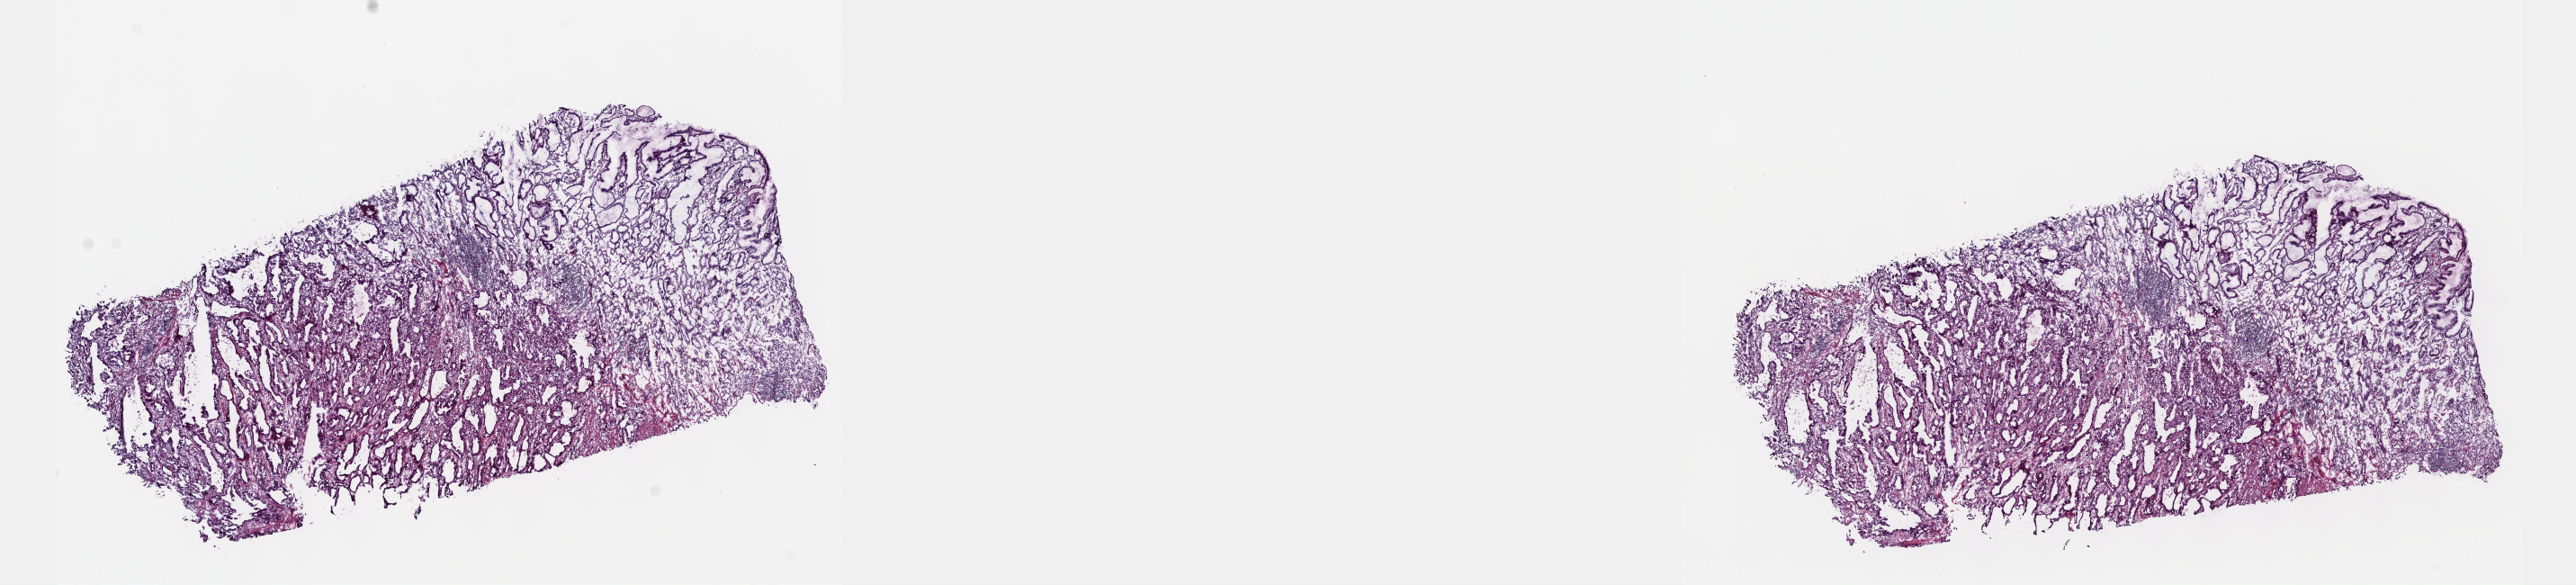
Digitized H&E tissue section (whole slide), shown as a low-resolution overview of the whole scanned area (about 23.1 x 5.3 mm, from a 40x scan); frozen section; primary tumour sample from the stomach. Male, age 76 years at initial diagnosis. Histologic grade: G2 (moderately differentiated). Composition of this section per pathologist review: tumour cells 100%, tumour nuclei 65%, normal cells 0%, stromal cells 0%, necrosis 0%. Infiltration values recorded for this section: lymphocyte infiltration 4%, monocyte infiltration 0%, neutrophil infiltration 0%.
Histologic diagnosis: Adenocarcinoma, intestinal type. AJCC pathologic stage: IIIA (6th edition).